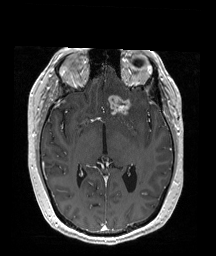
Brain MRI from a brain-tumour surgery series, one axial slice; position 103 of 192 along the scan axis; T1-weighted post-contrast; 216 × 256 image matrix, field of view 211 × 250 mm. From the clinical record (not read from this slice): histopathology: Oligodendroglioma; WHO grade: 2; IDH mutation: yes.
Annotated regions visible in this slice (outlined manually by an expert reader):
- tumour: bounding box [x1, y1, x2, y2] px = [107, 95, 132, 117]